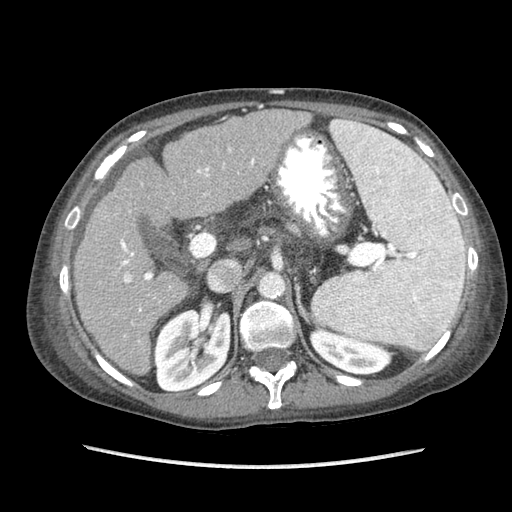
Contrast-enhanced abdominal CT (liver protocol), one axial slice; slice 47 of 87 in the series (ordered by position); soft-tissue window (W 400 / L 40 HU); 2.5 mm slice thickness; 512 × 512 image matrix, field of view 340 × 340 mm. From the clinical record (not read from this slice): diagnosis: hepatocellular carcinoma (patient treated with transarterial chemoembolisation; whether this scan precedes or follows treatment is not stated here); TNM stage (as recorded): Stage-IIIB; Child-Pugh class: A; tumour differentiation: no biopsy; tumour nodularity: uninodular.
Structures marked on this image (semi-automatic segmentation, software-assisted and operator-edited):
- liver parenchyma outside the tumour (the mass and vessels are separate outlines, so this box may not span the whole liver): bounding box (x1, y1, x2, y2) in pixels: (74, 110, 310, 374)
- liver vessels: (120, 149, 254, 312)